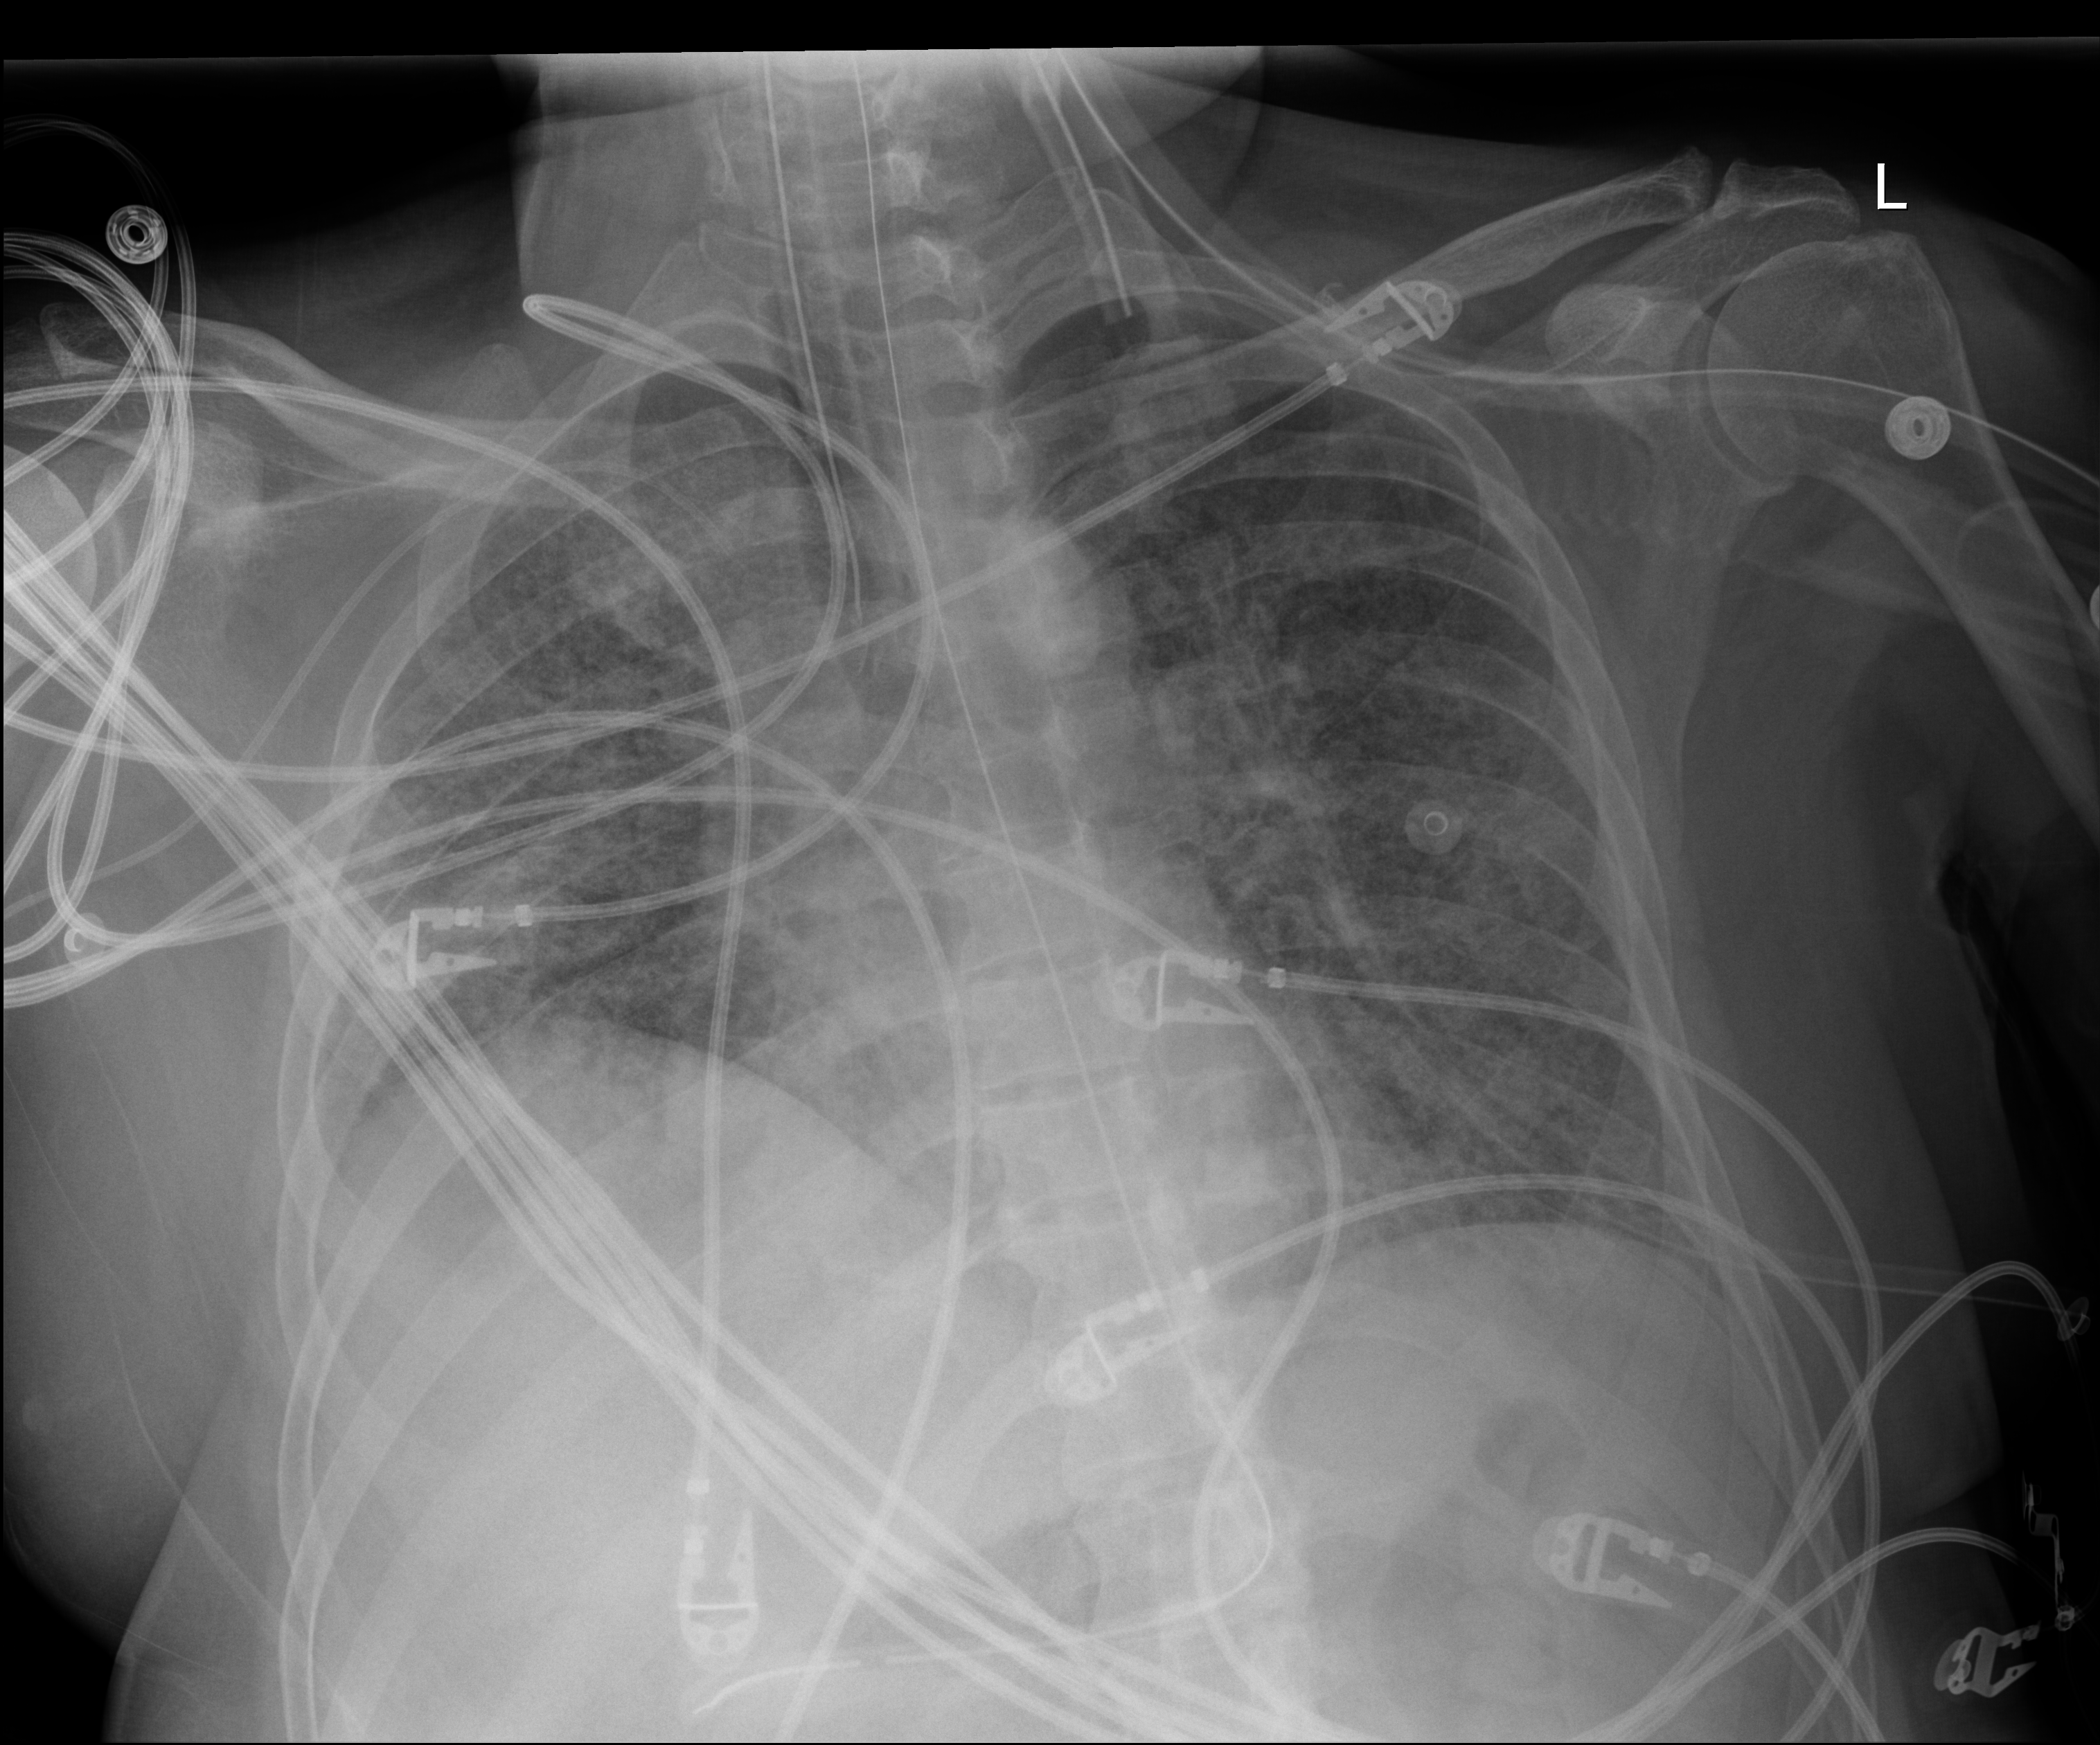
Bedside chest radiograph (digital radiography). Male patient hospitalised with COVID-19, age 18–59 years.
Hospital-stay facts (about this admission, not read from this image; timing relative to this image not recorded):
- admitted to intensive care during this hospital stay: yes